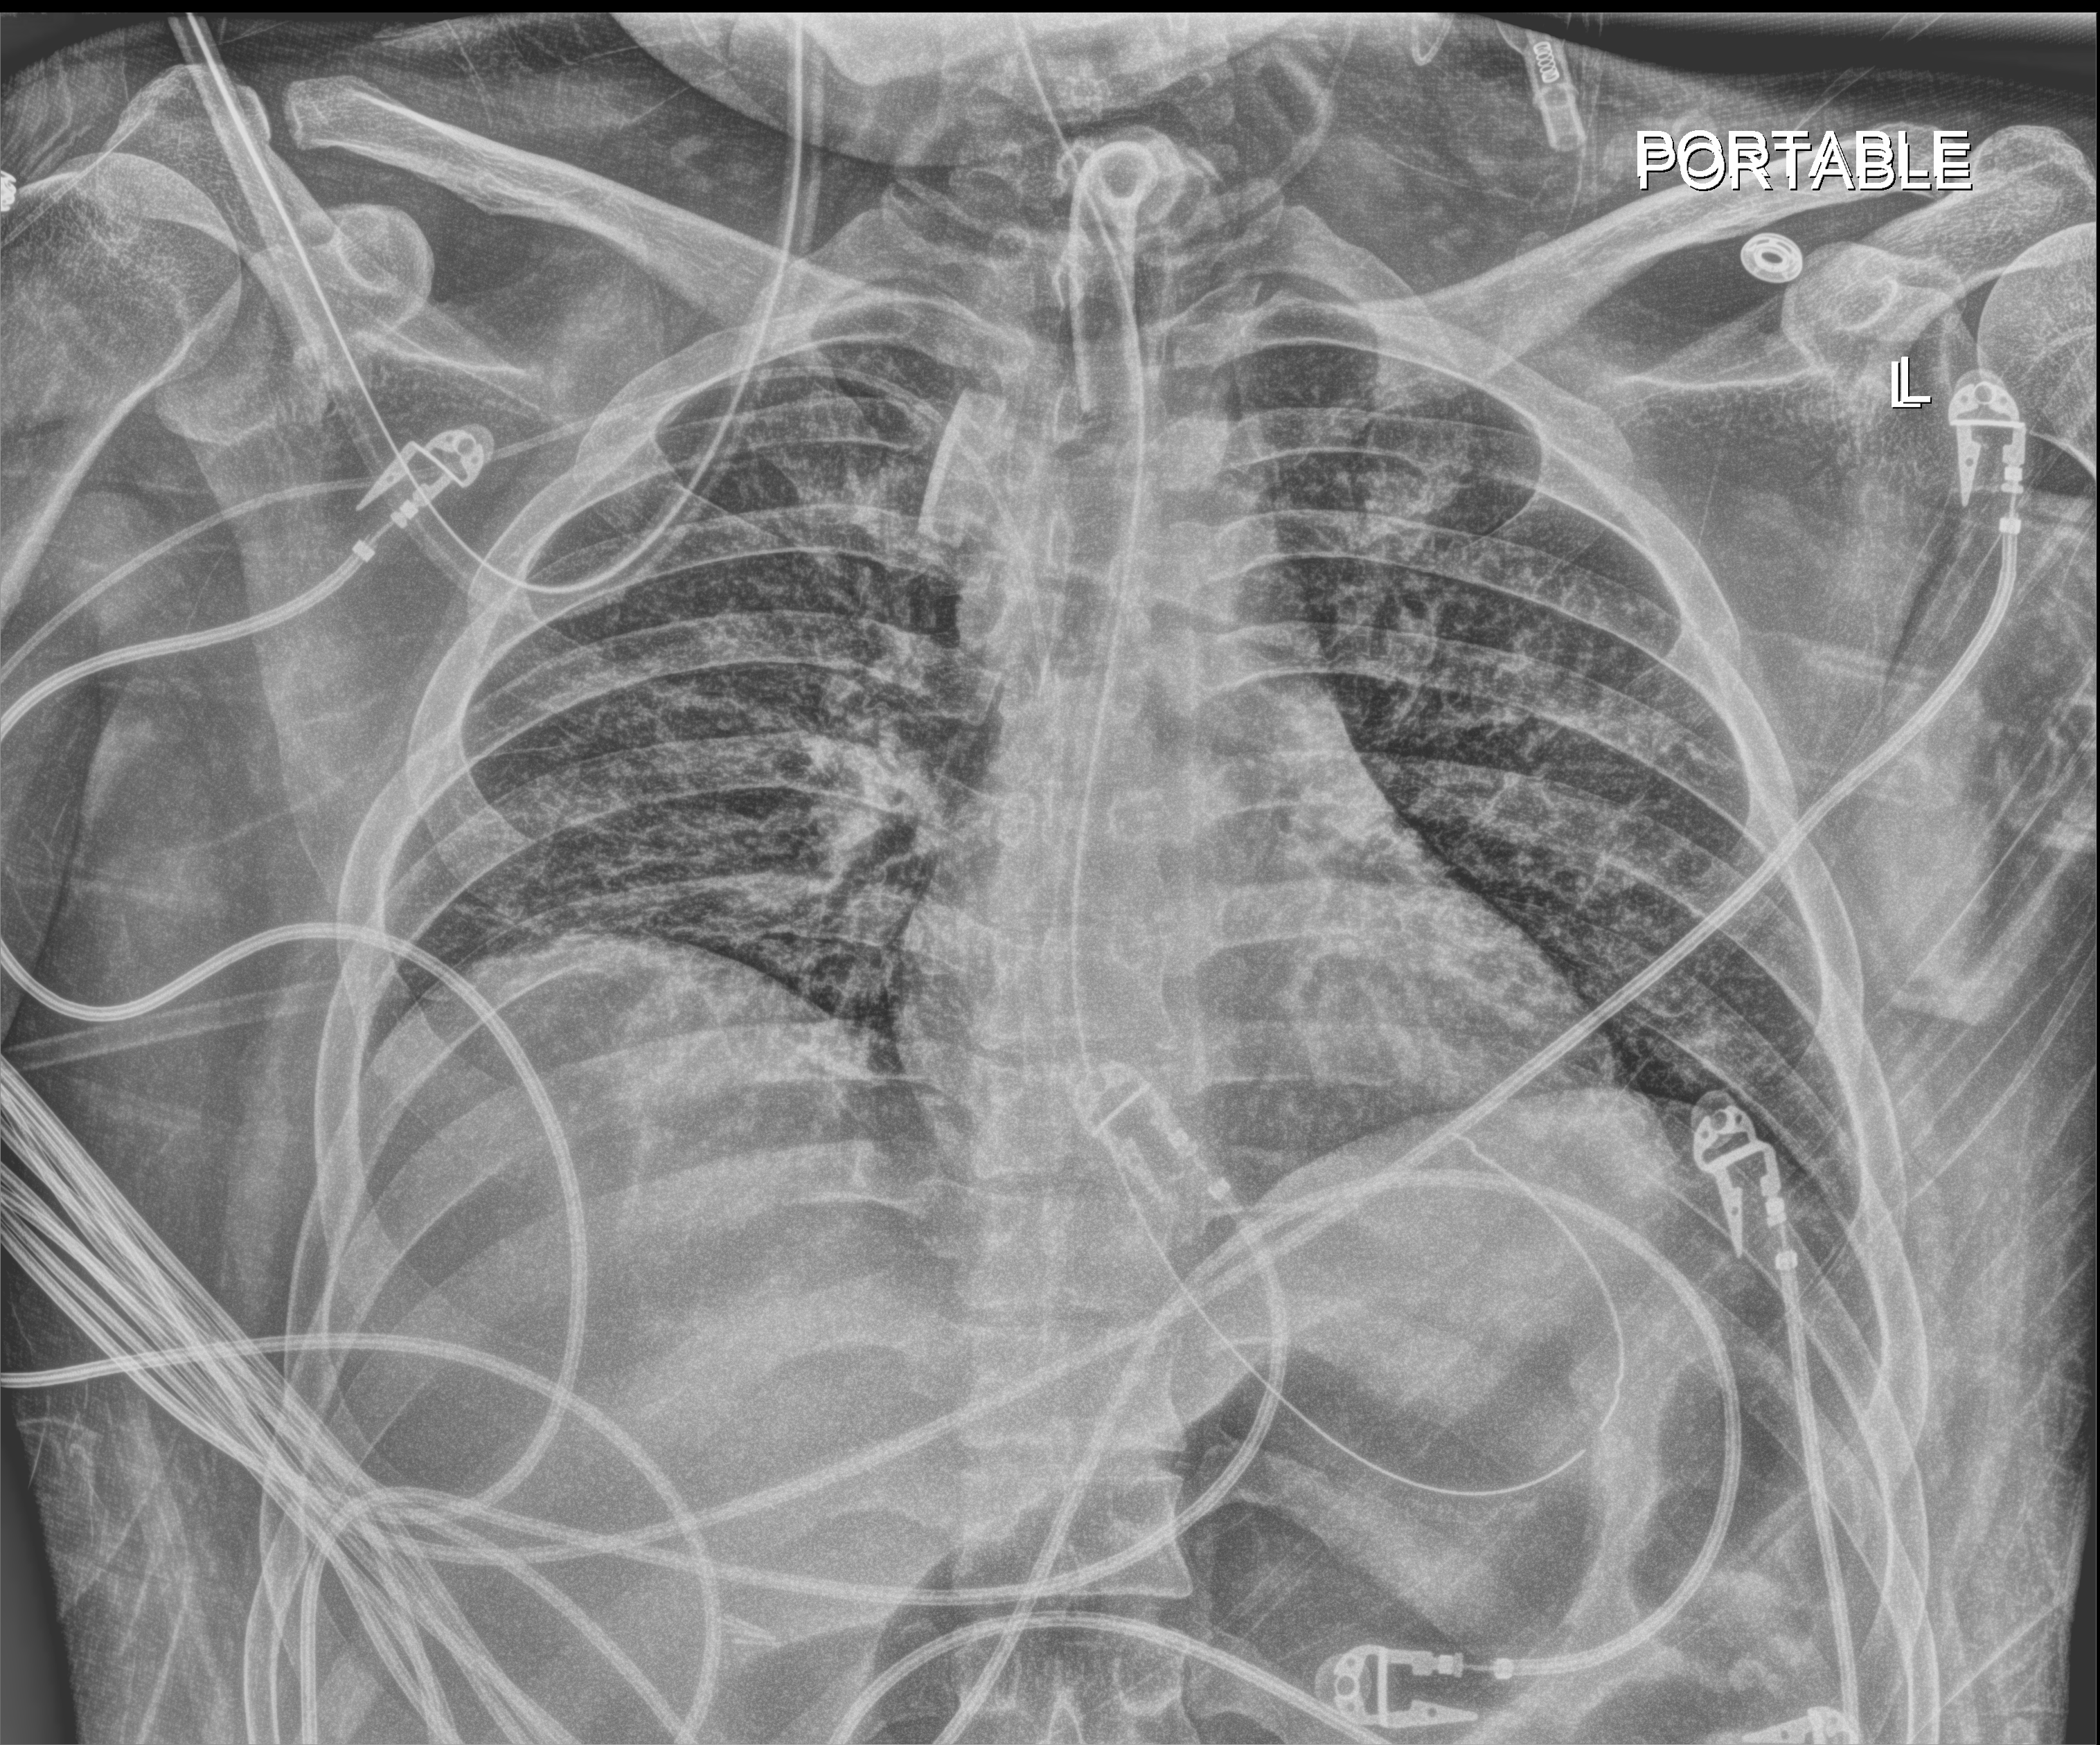
Chest radiograph (digital radiography), anteroposterior (AP) projection. Male patient hospitalised with COVID-19, age 18–59 years.
From the hospital-stay record, not from the radiograph (when in the stay this image was taken is not recorded): admitted to intensive care during this hospital stay: yes; mechanically ventilated during this hospital stay: yes.